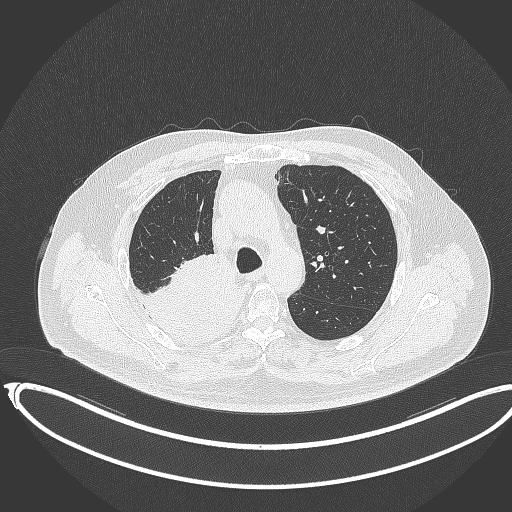
Chest CT, one axial slice. Position 257 of 403 along the scan axis. Reconstruction kernel B70f. 120 kVp. Lung window (W 1500 / L -600 HU). 512 × 512 image matrix, field of view 436 × 436 mm. Male patient, age 68 years. From the clinical record (not read from this slice): clinical TNM (as recorded): T2a N0 M0.
Structures marked on this image (rectangle marked by the reading radiologist):
- lung tumour (recorded histology: adenocarcinoma): bounding box [x1, y1, x2, y2] px = [132, 259, 254, 353]